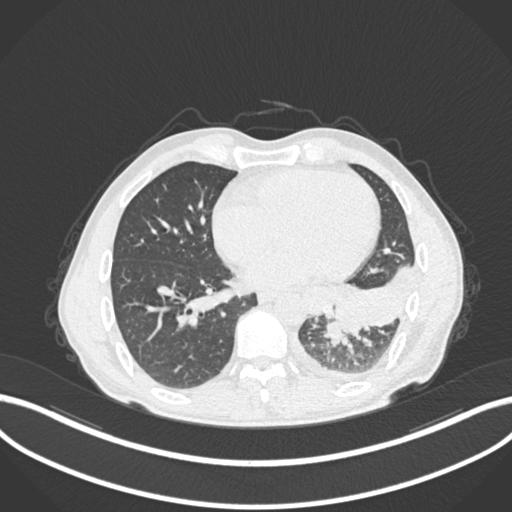
Chest CT, one axial slice. Slice 90 of 222 in the series (ordered by position). Reconstruction kernel B30f. Lung window (W 1500 / L -600 HU). 1 mm slice thickness. 512 × 512 image matrix, field of view 400 × 400 mm. Male patient, age 47 years. From the clinical record (not read from this slice): clinical TNM (as recorded): T3 N1 M1c; histopathological grade: G3.
Structures marked on this image (bounding box drawn by a radiologist):
- lung tumour (recorded histology: small cell carcinoma): bounding box (x1, y1, x2, y2) in pixels: (321, 319, 353, 350)